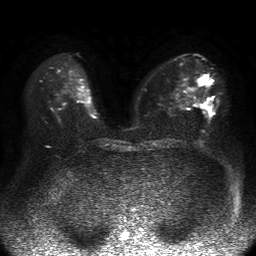
Breast MRI, one axial slice. Position 28 of 50 along the scan axis. Diffusion-weighted series; image 2 of 4 stored at this slice position (different b-values; order by instance number). 1.5 T. 4 mm slice thickness. 256 × 256 image matrix, field of view 360 × 360 mm. Female patient.
Structures marked on this image (outlined manually by an expert reader):
- tumour on diffusion-weighted imaging: bounding box <200,76,211,109> (left, top, right, bottom; pixels)